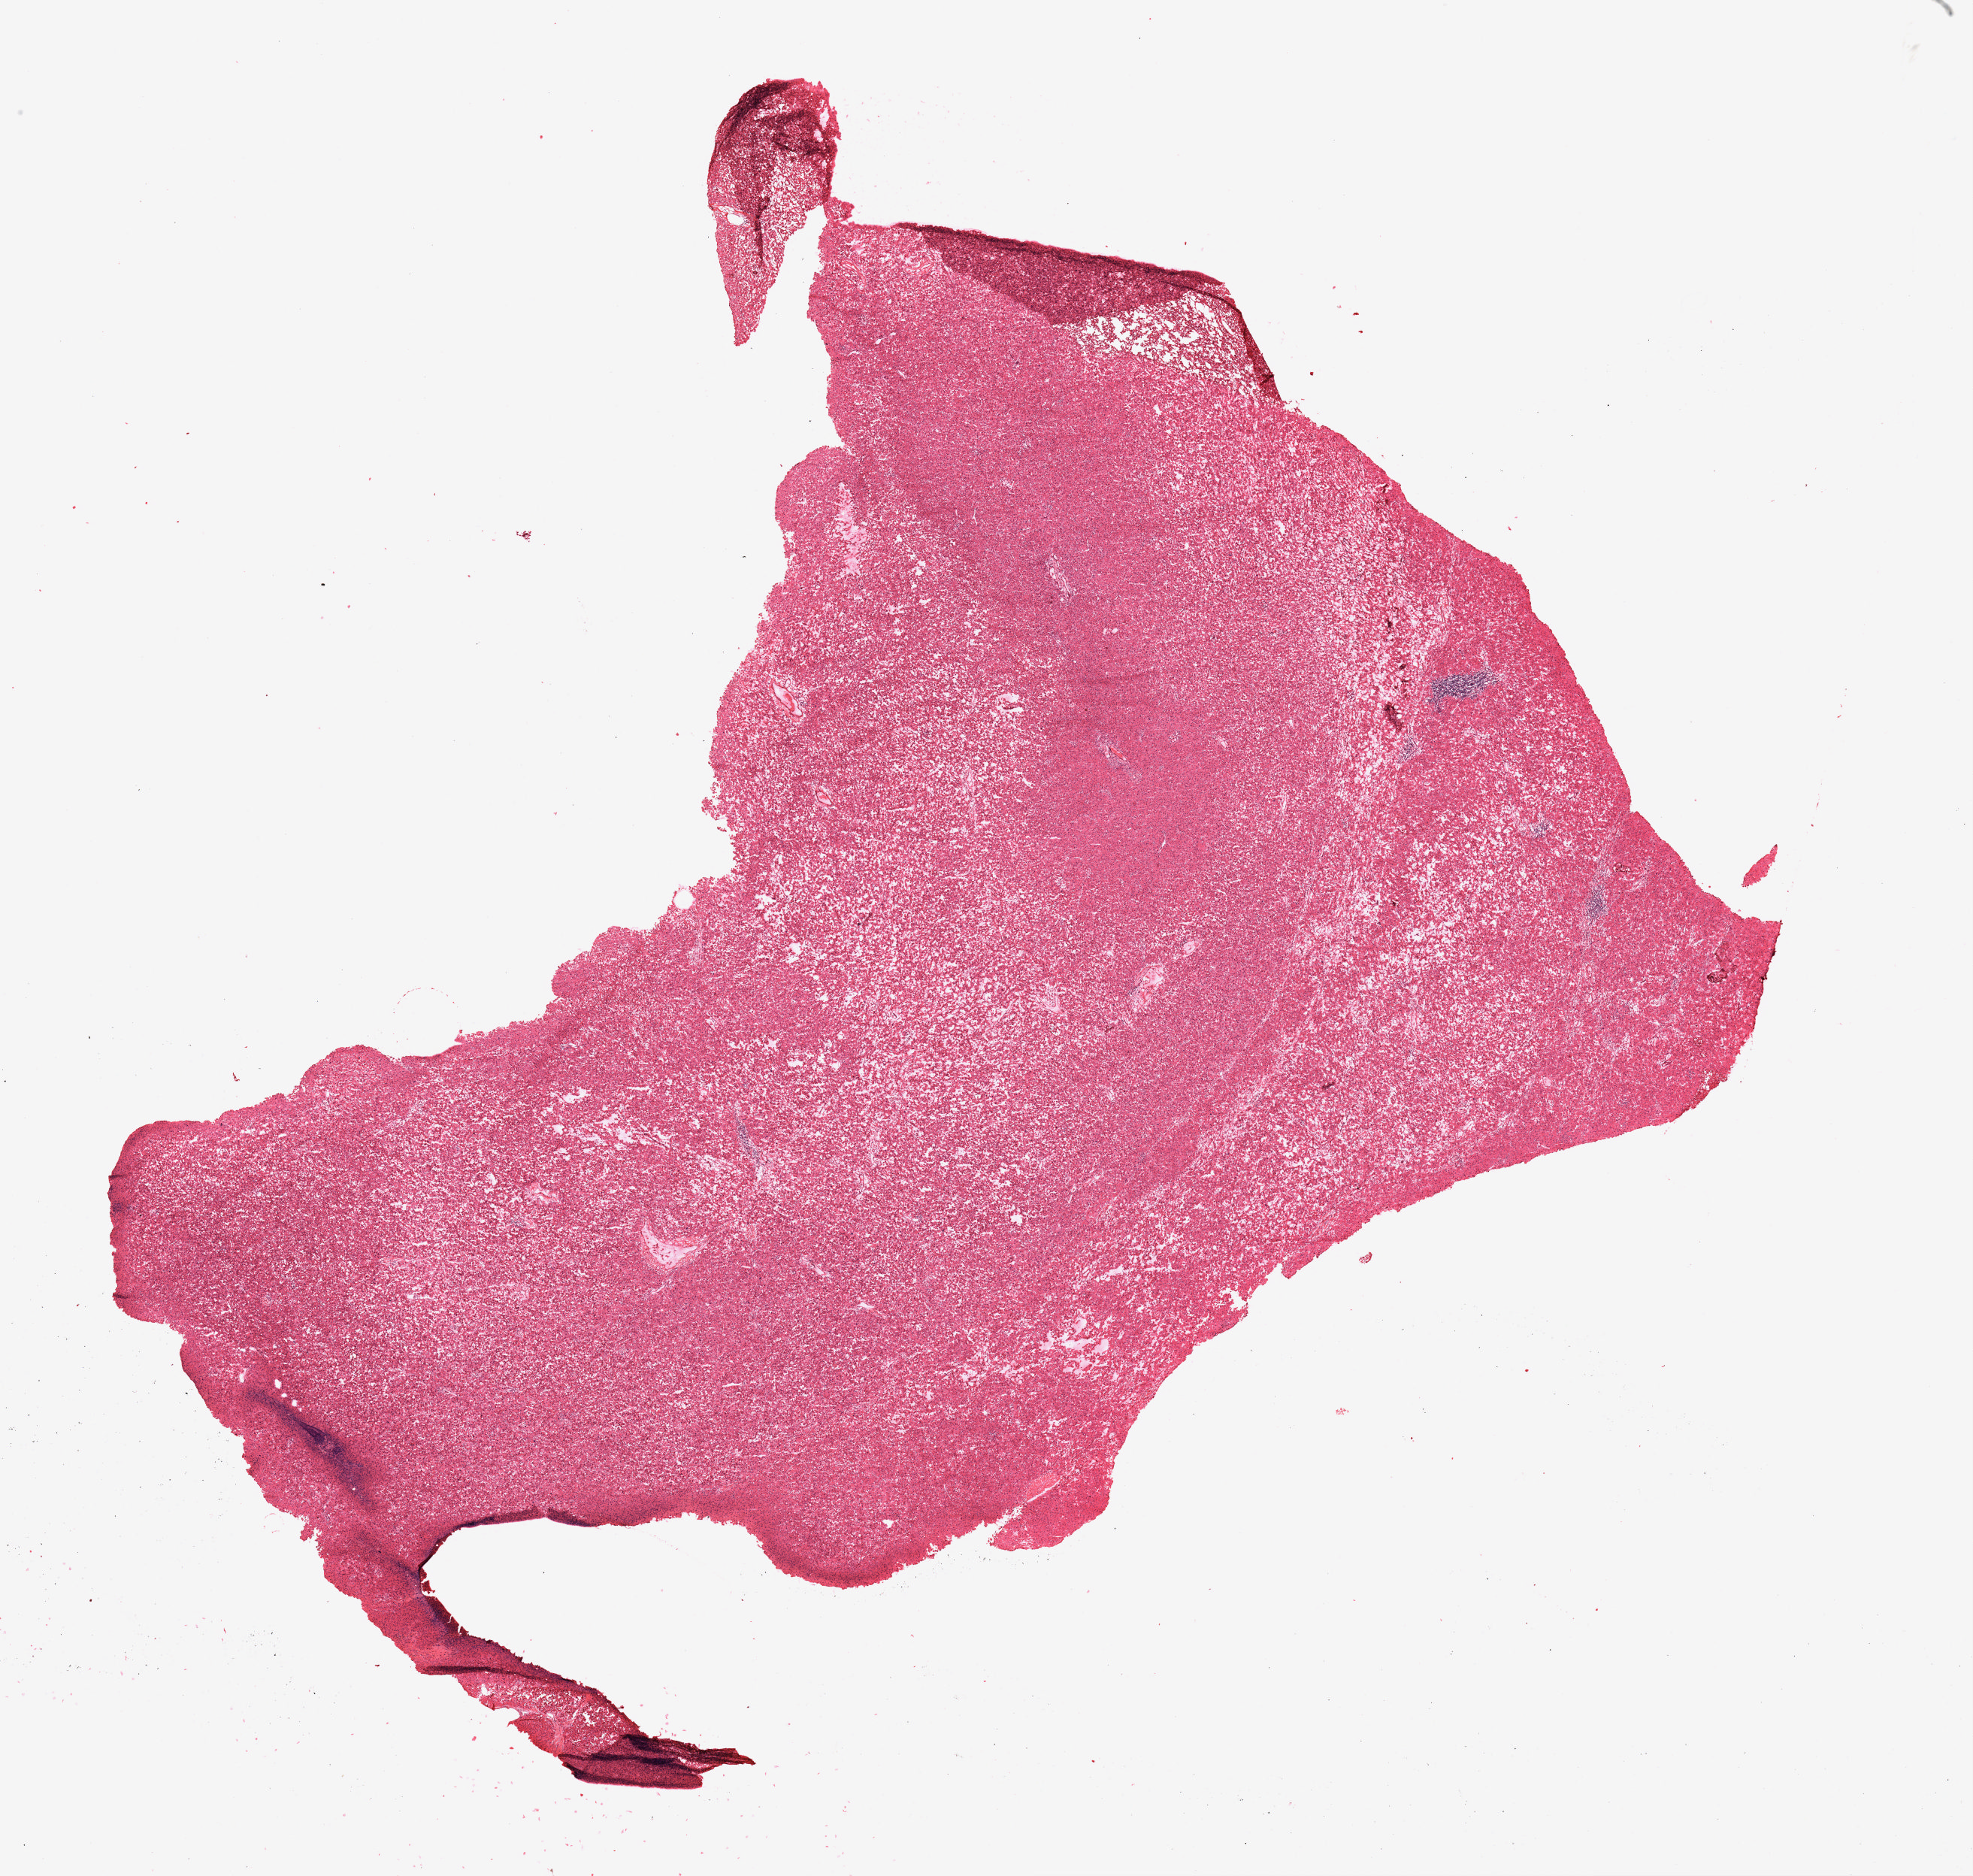
H&E whole-slide image, a low-resolution overview of the entire scanned area, about 21.0 x 19.9 mm, formalin-fixed paraffin-embedded (FFPE) diagnostic section, primary tumour sample from the adrenal cortex. Male, age 51 years at initial diagnosis.
Pathologic diagnosis: Adrenal cortical carcinoma.